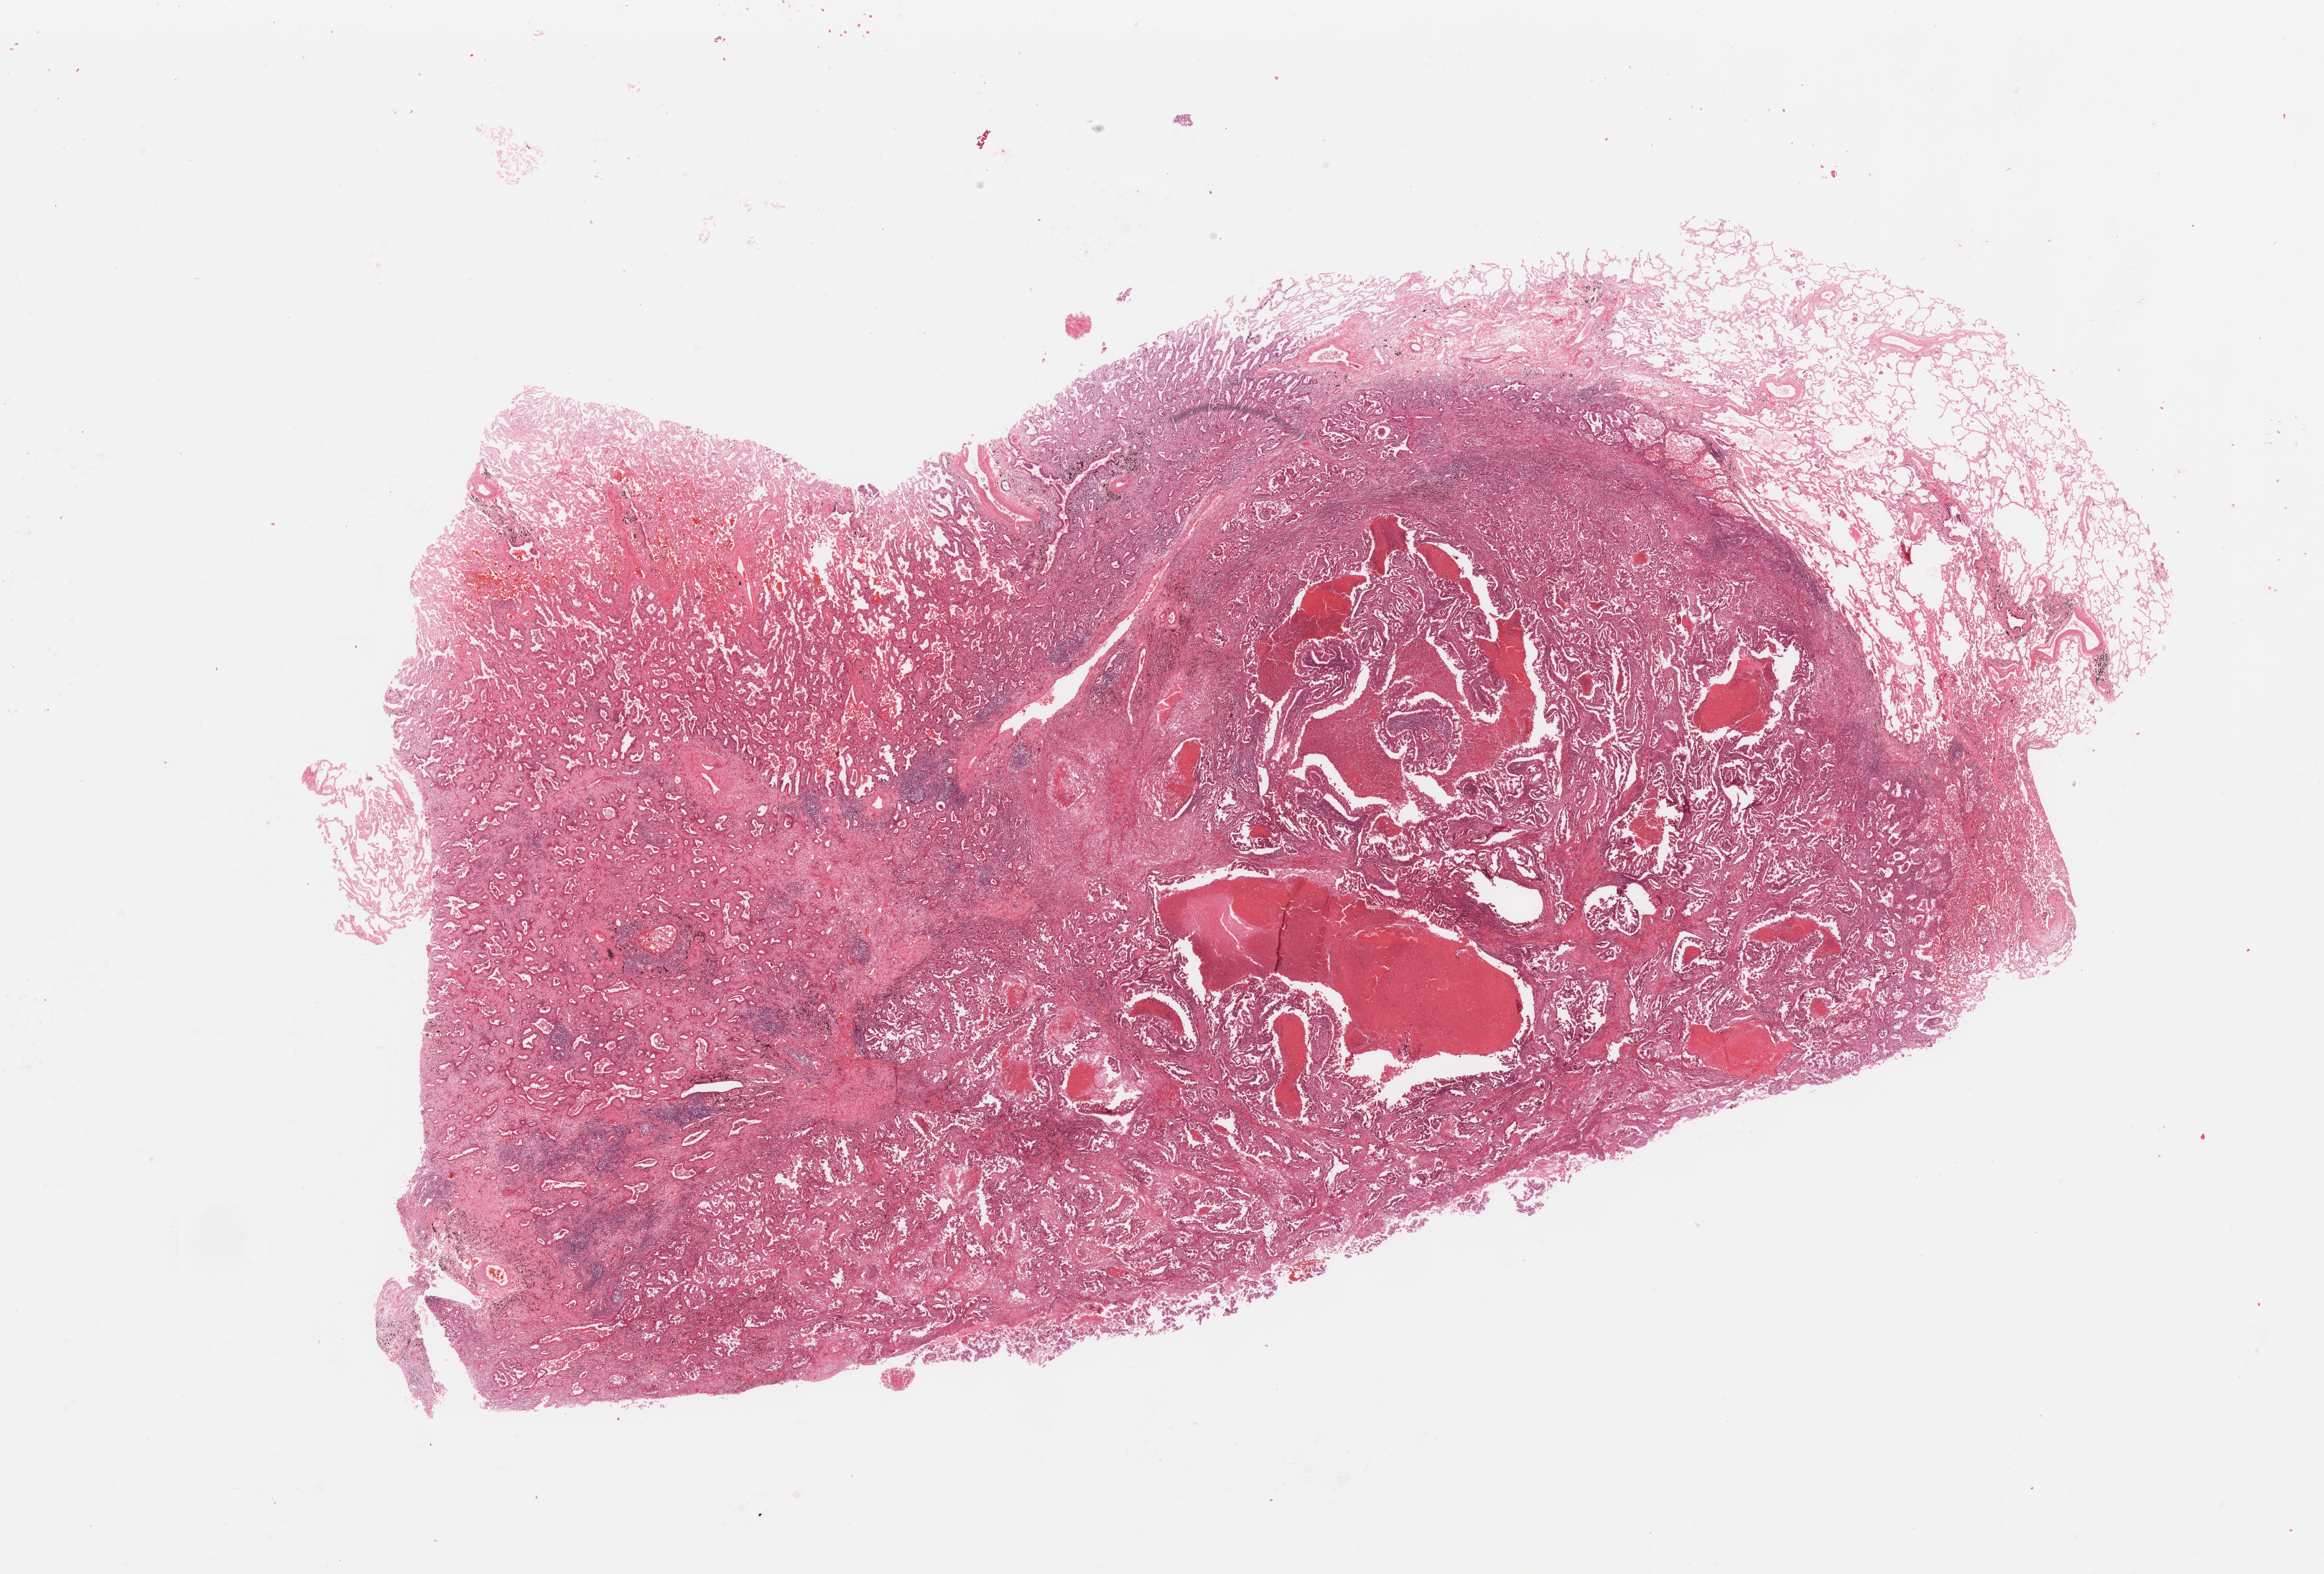
H&E whole-slide image, a low-resolution overview of the entire scanned area, about 25.6 x 17.3 mm, tumour tissue sample, lung. 67-year-old female patient. Histologic grade: G2 (moderately differentiated).
AJCC pathologic stage: IIIA. Histologic diagnosis: Adenocarcinoma, NOS.